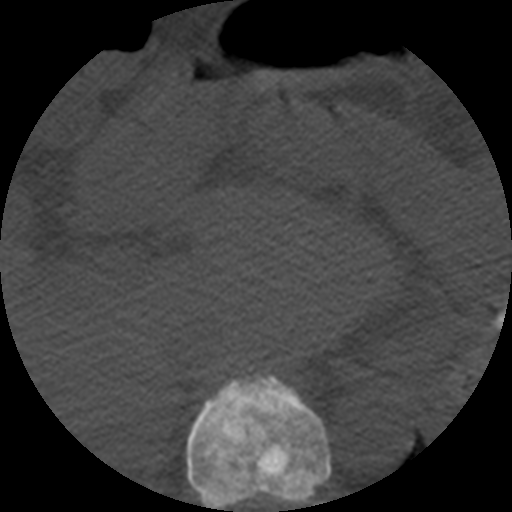
CT including the spine, one axial slice; position 258 of 508 along the scan axis; 120 kVp; bone window (W 1800 / L 400 HU); 1.25 mm slice thickness; 512 × 512 image matrix, field of view 160 × 160 mm. Patient age 57 years. From the clinical record (not read from this slice): primary cancer: prostate.
Outlined on this slice (semi-automatically segmented with operator editing):
- T10 vertebra: bounding box (x1, y1, x2, y2) in pixels: (187, 373, 331, 512)